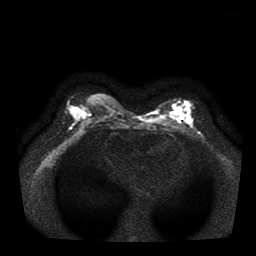
Breast MRI, one axial slice. Slice 14 of 35 in the series (ordered by position). Diffusion-weighted series; image 2 of 4 stored at this slice position (different b-values; order by instance number). 1.5 T. 5 mm slice thickness. 256 × 256 image matrix, field of view 330 × 330 mm. Female patient.
Outlined on this slice (expert manual segmentation):
- tumour on diffusion-weighted imaging: box from (x=175, y=107) to (x=180, y=114) px